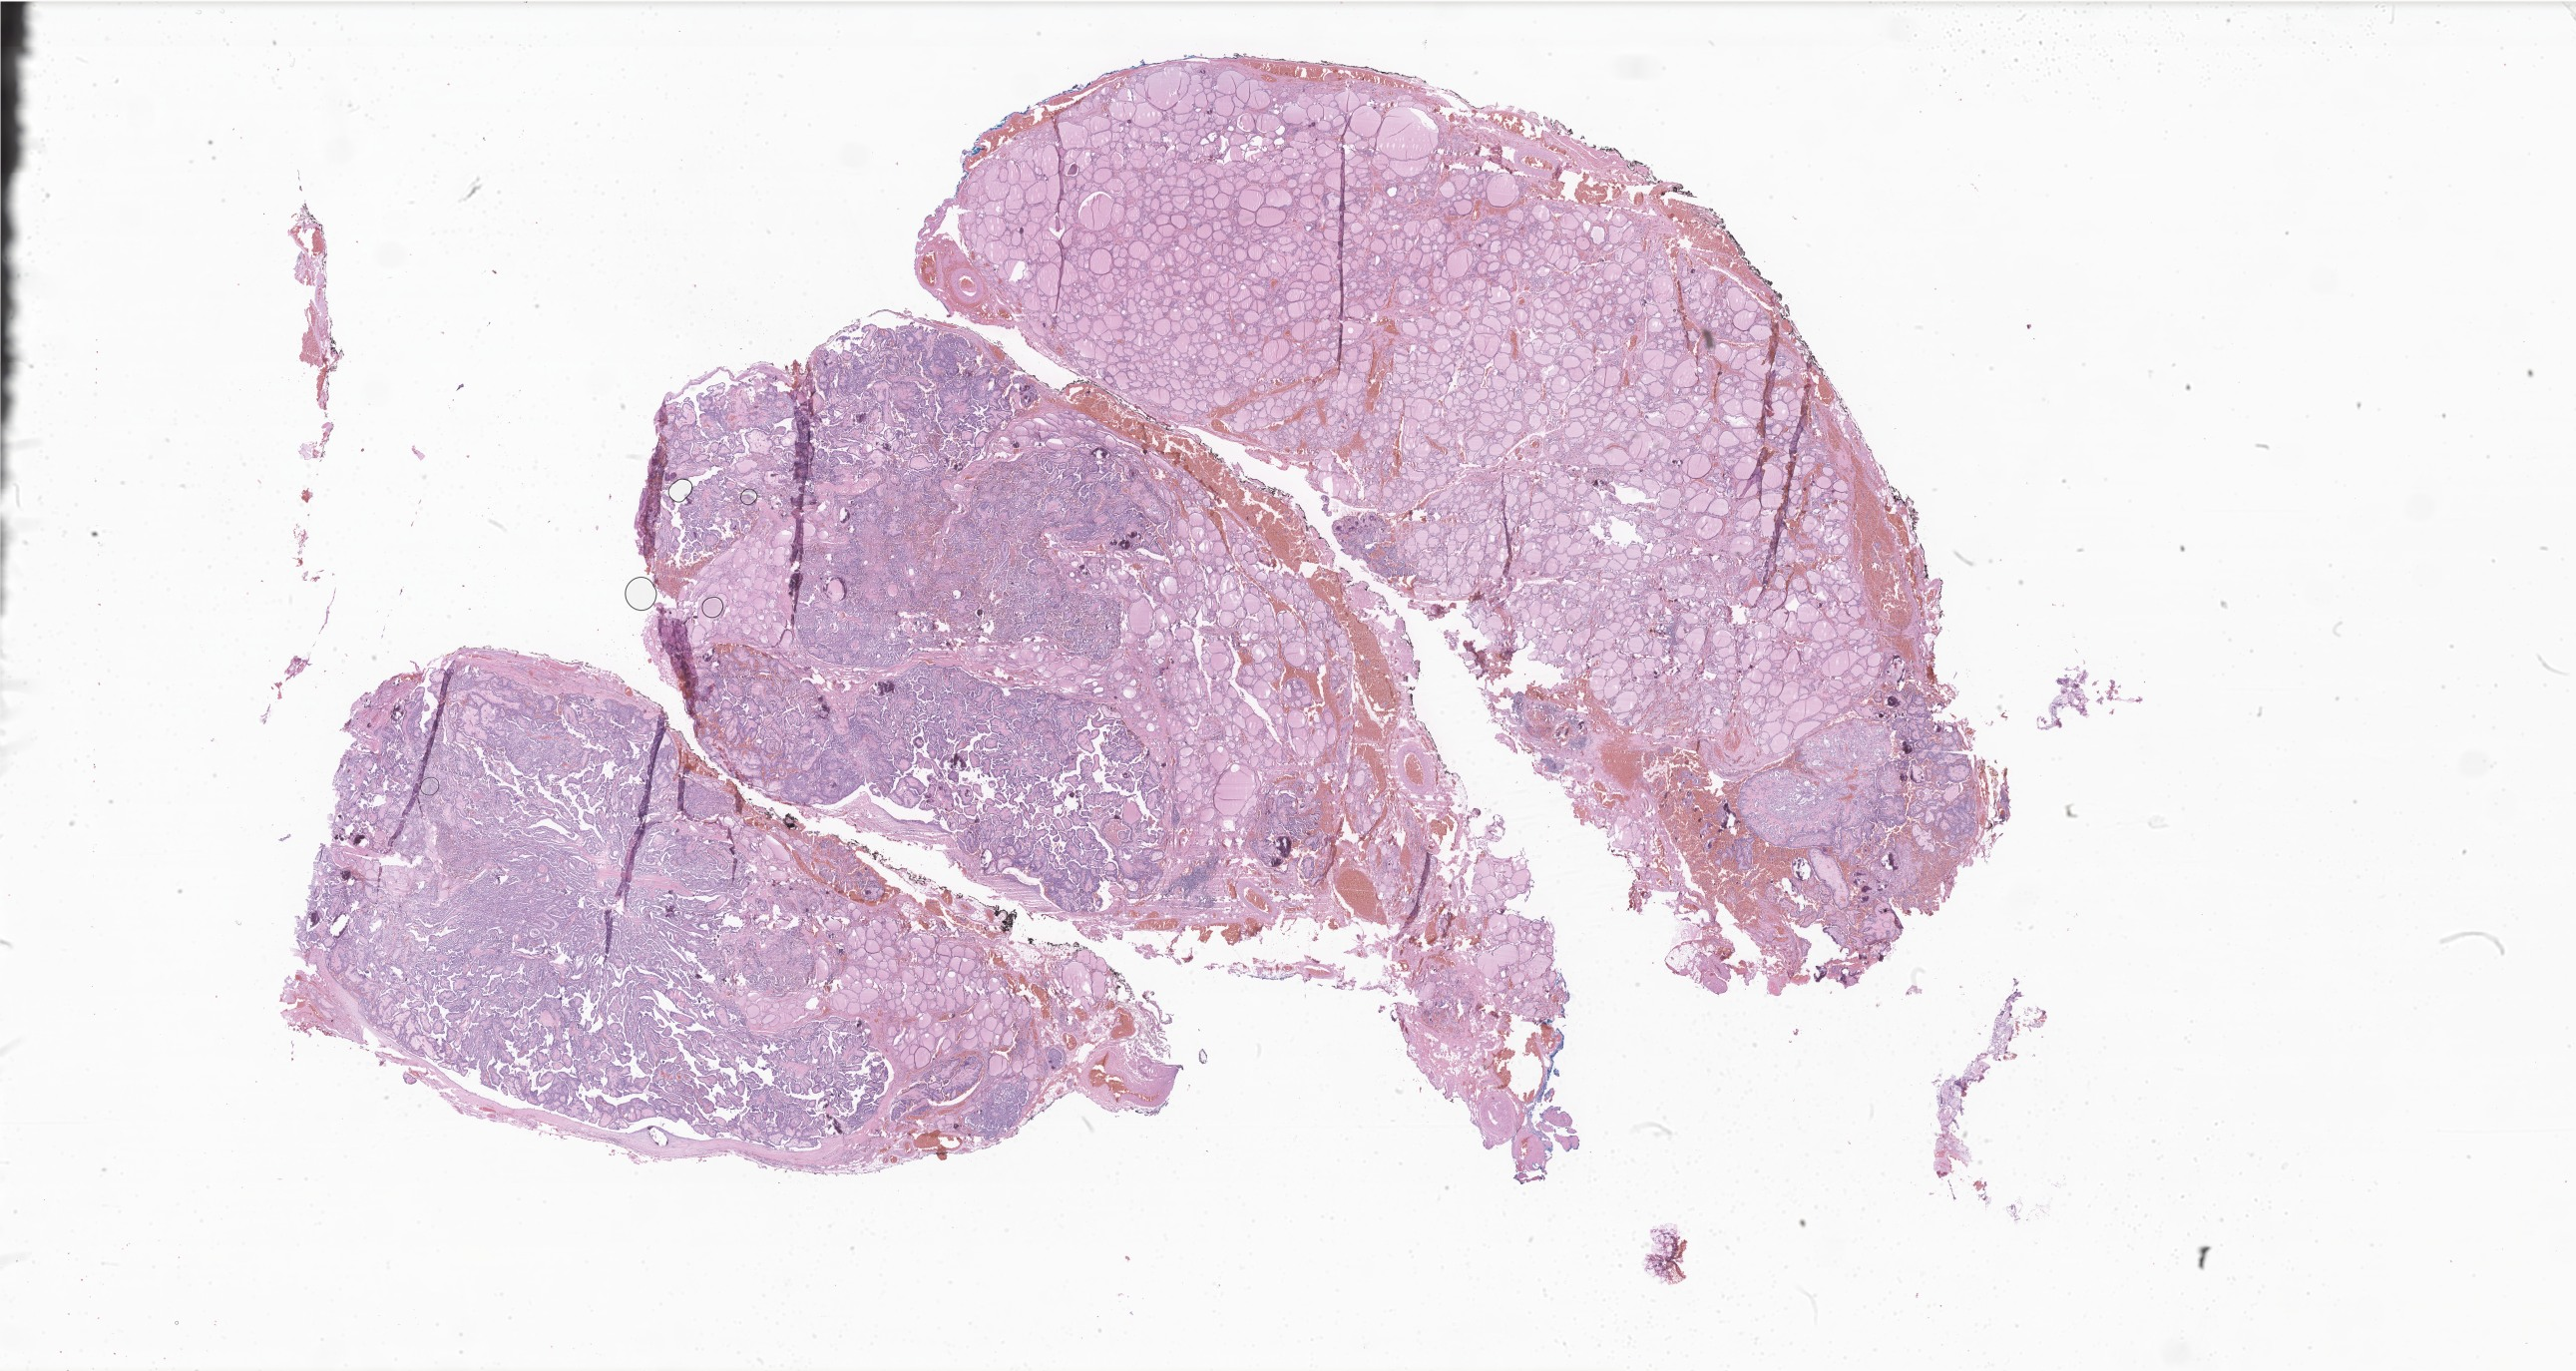
Whole-slide image, haematoxylin and eosin stain of tumor tissue from the thyroid, whole scanned area (about 43.6 x 23.2 mm) shown as a low-resolution overview. Formalin-fixed paraffin-embedded section. Patient: female, age 219 months (18 years 3 months).
Diagnosis: Papillary carcinoma, NOS.